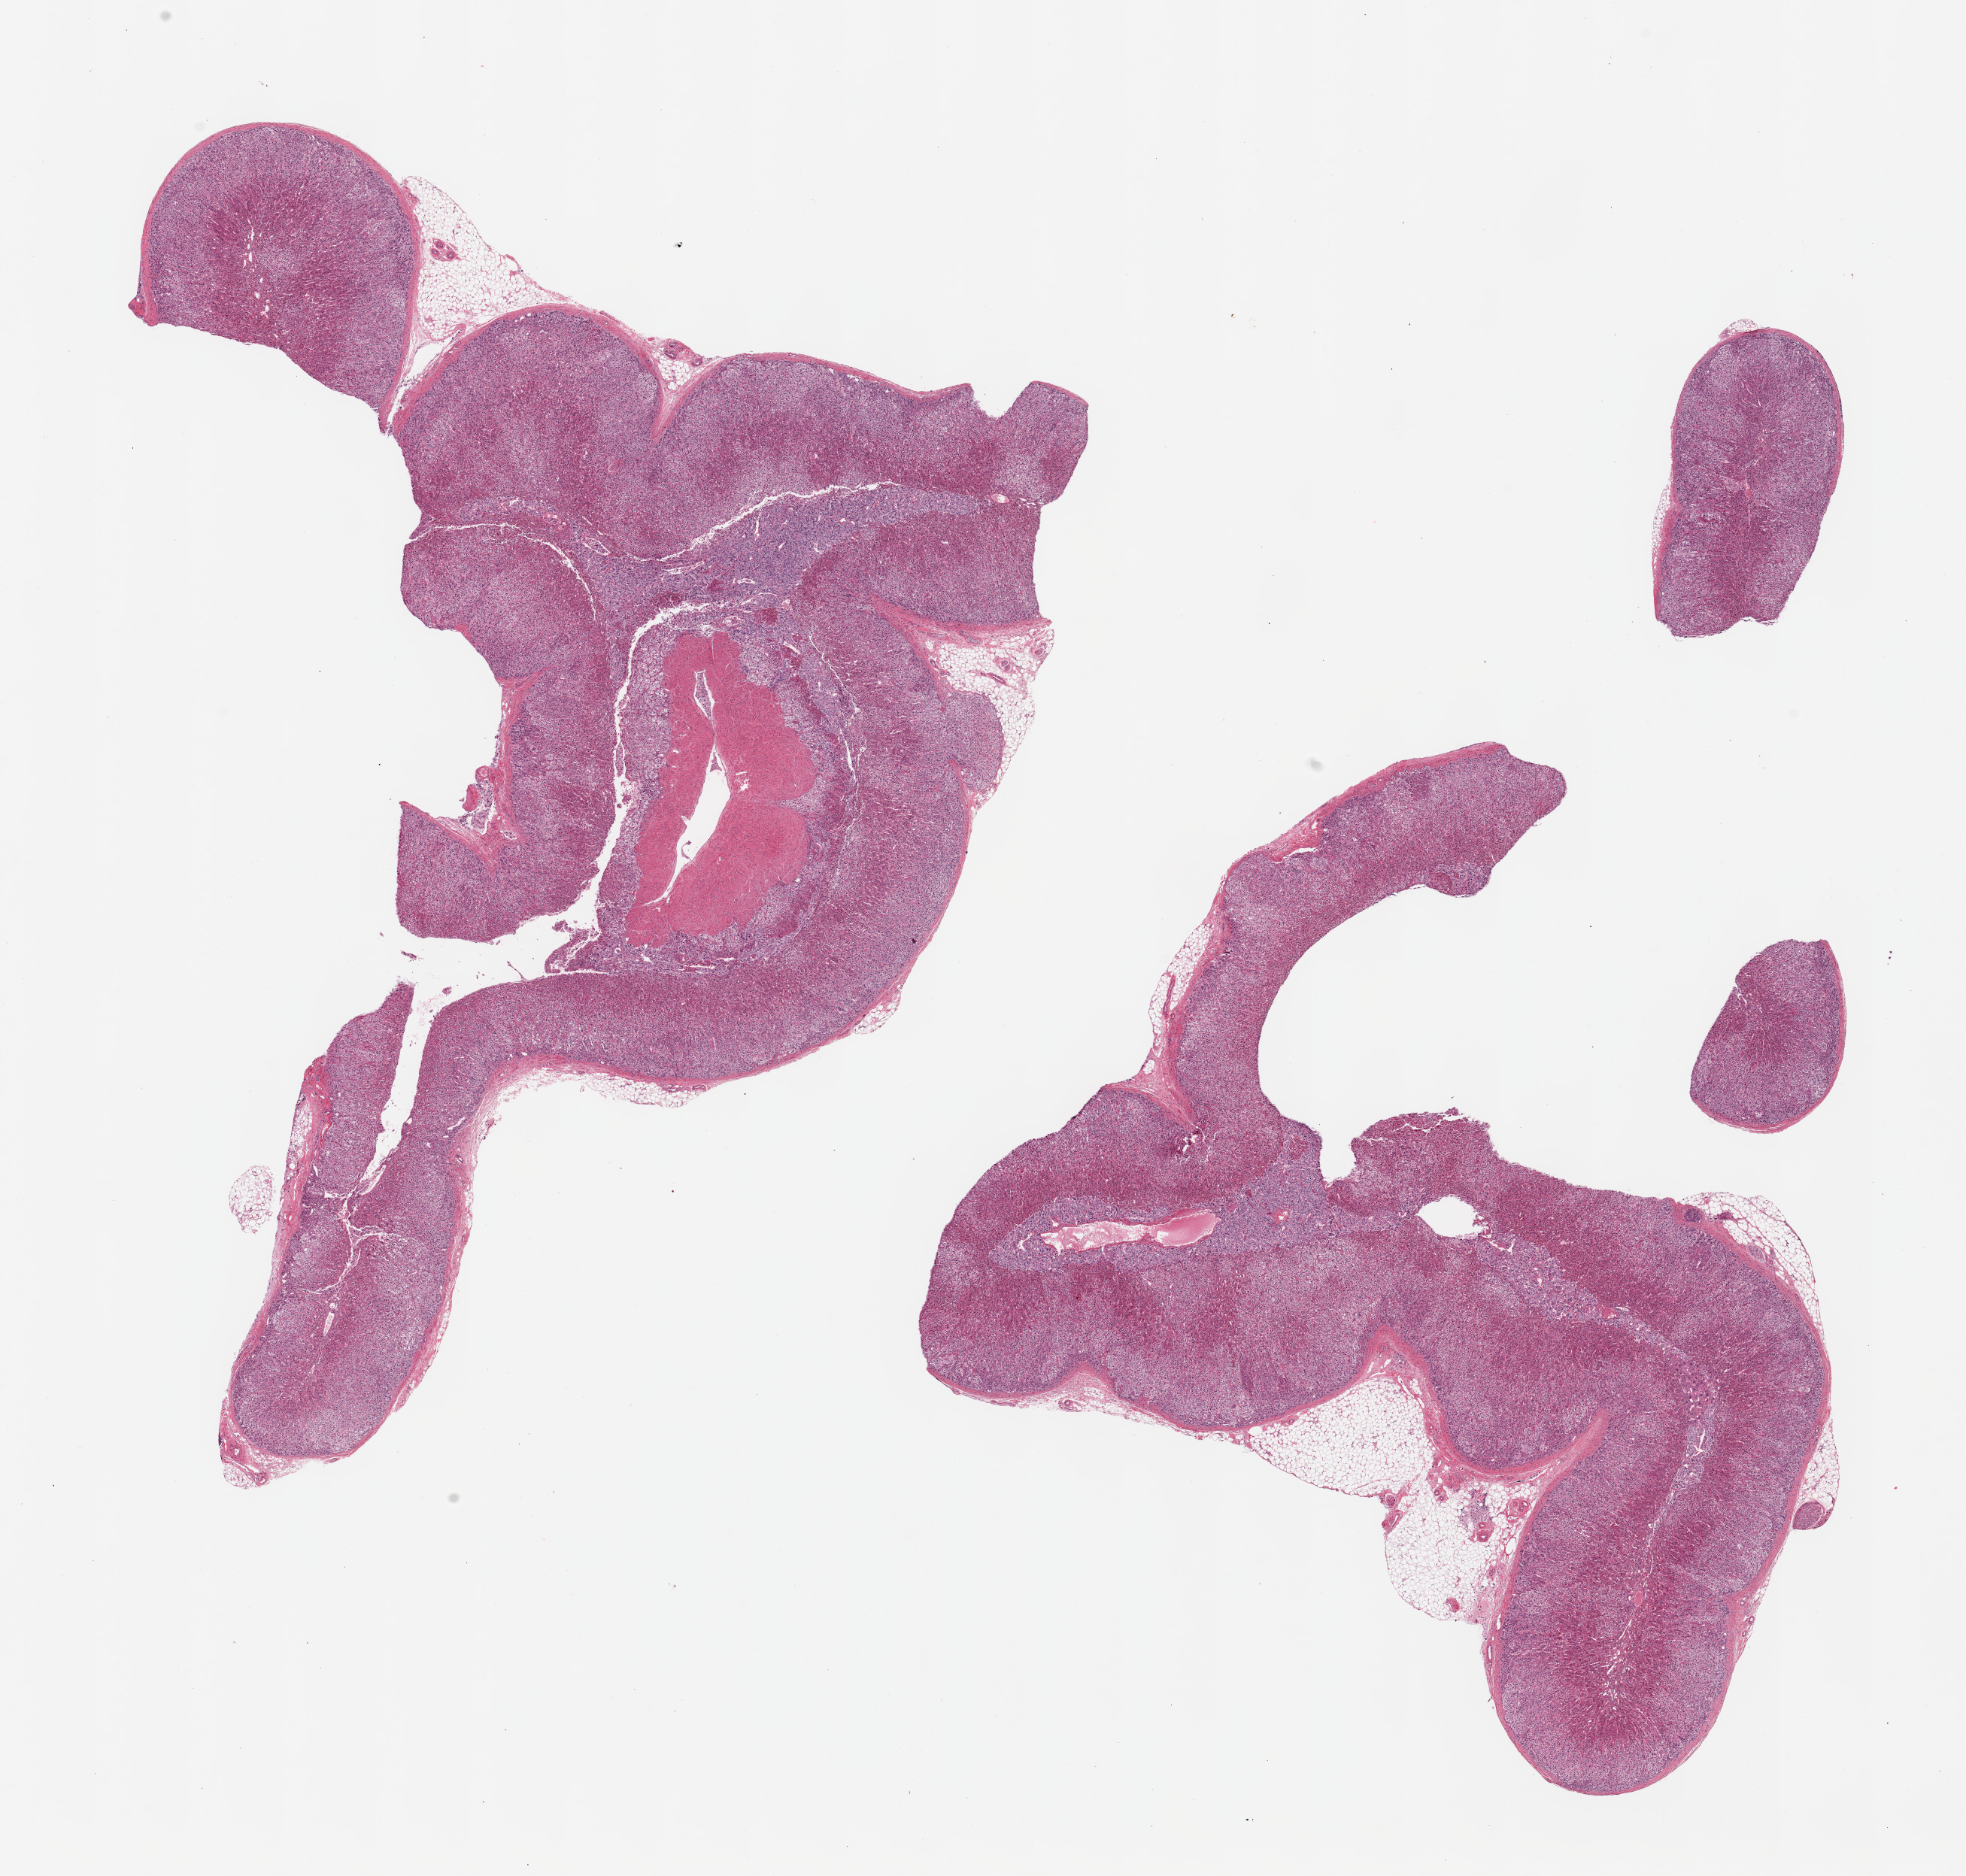
Digitized haematoxylin and eosin-stained section, brightfield — shown as a low-resolution overview of the whole scanned area (about 20.7 x 19.7 mm, from a 20x scan). PAXgene-fixed paraffin-embedded (PFPE) section. Section of adrenal gland (target tissue). Donor tissue sample. Donor sex: female.
* reviewer comment on this tissue sample: 2 pieces, medulla visible--valuable specimen; Trace fat by interrupted line